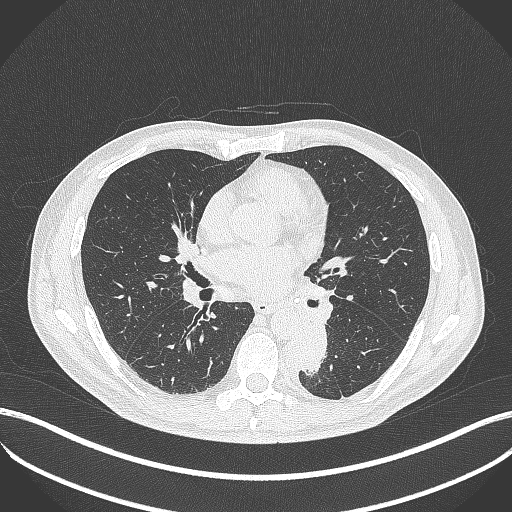
Chest CT, one axial slice. Position 207 of 451 along the scan axis. Reconstruction kernel B70f. 120 kVp. Lung window (W 1500 / L -600 HU). 512 × 512 image matrix, field of view 400 × 400 mm. Patient: male, 72 years. Case-level facts recorded for this patient, not image findings: clinical TNM (as recorded): T2b N0 M1.
Outlined on this slice (rectangle marked by the reading radiologist):
- lung tumour (recorded histology: adenocarcinoma): bounding box <280,321,332,384> (left, top, right, bottom; pixels)